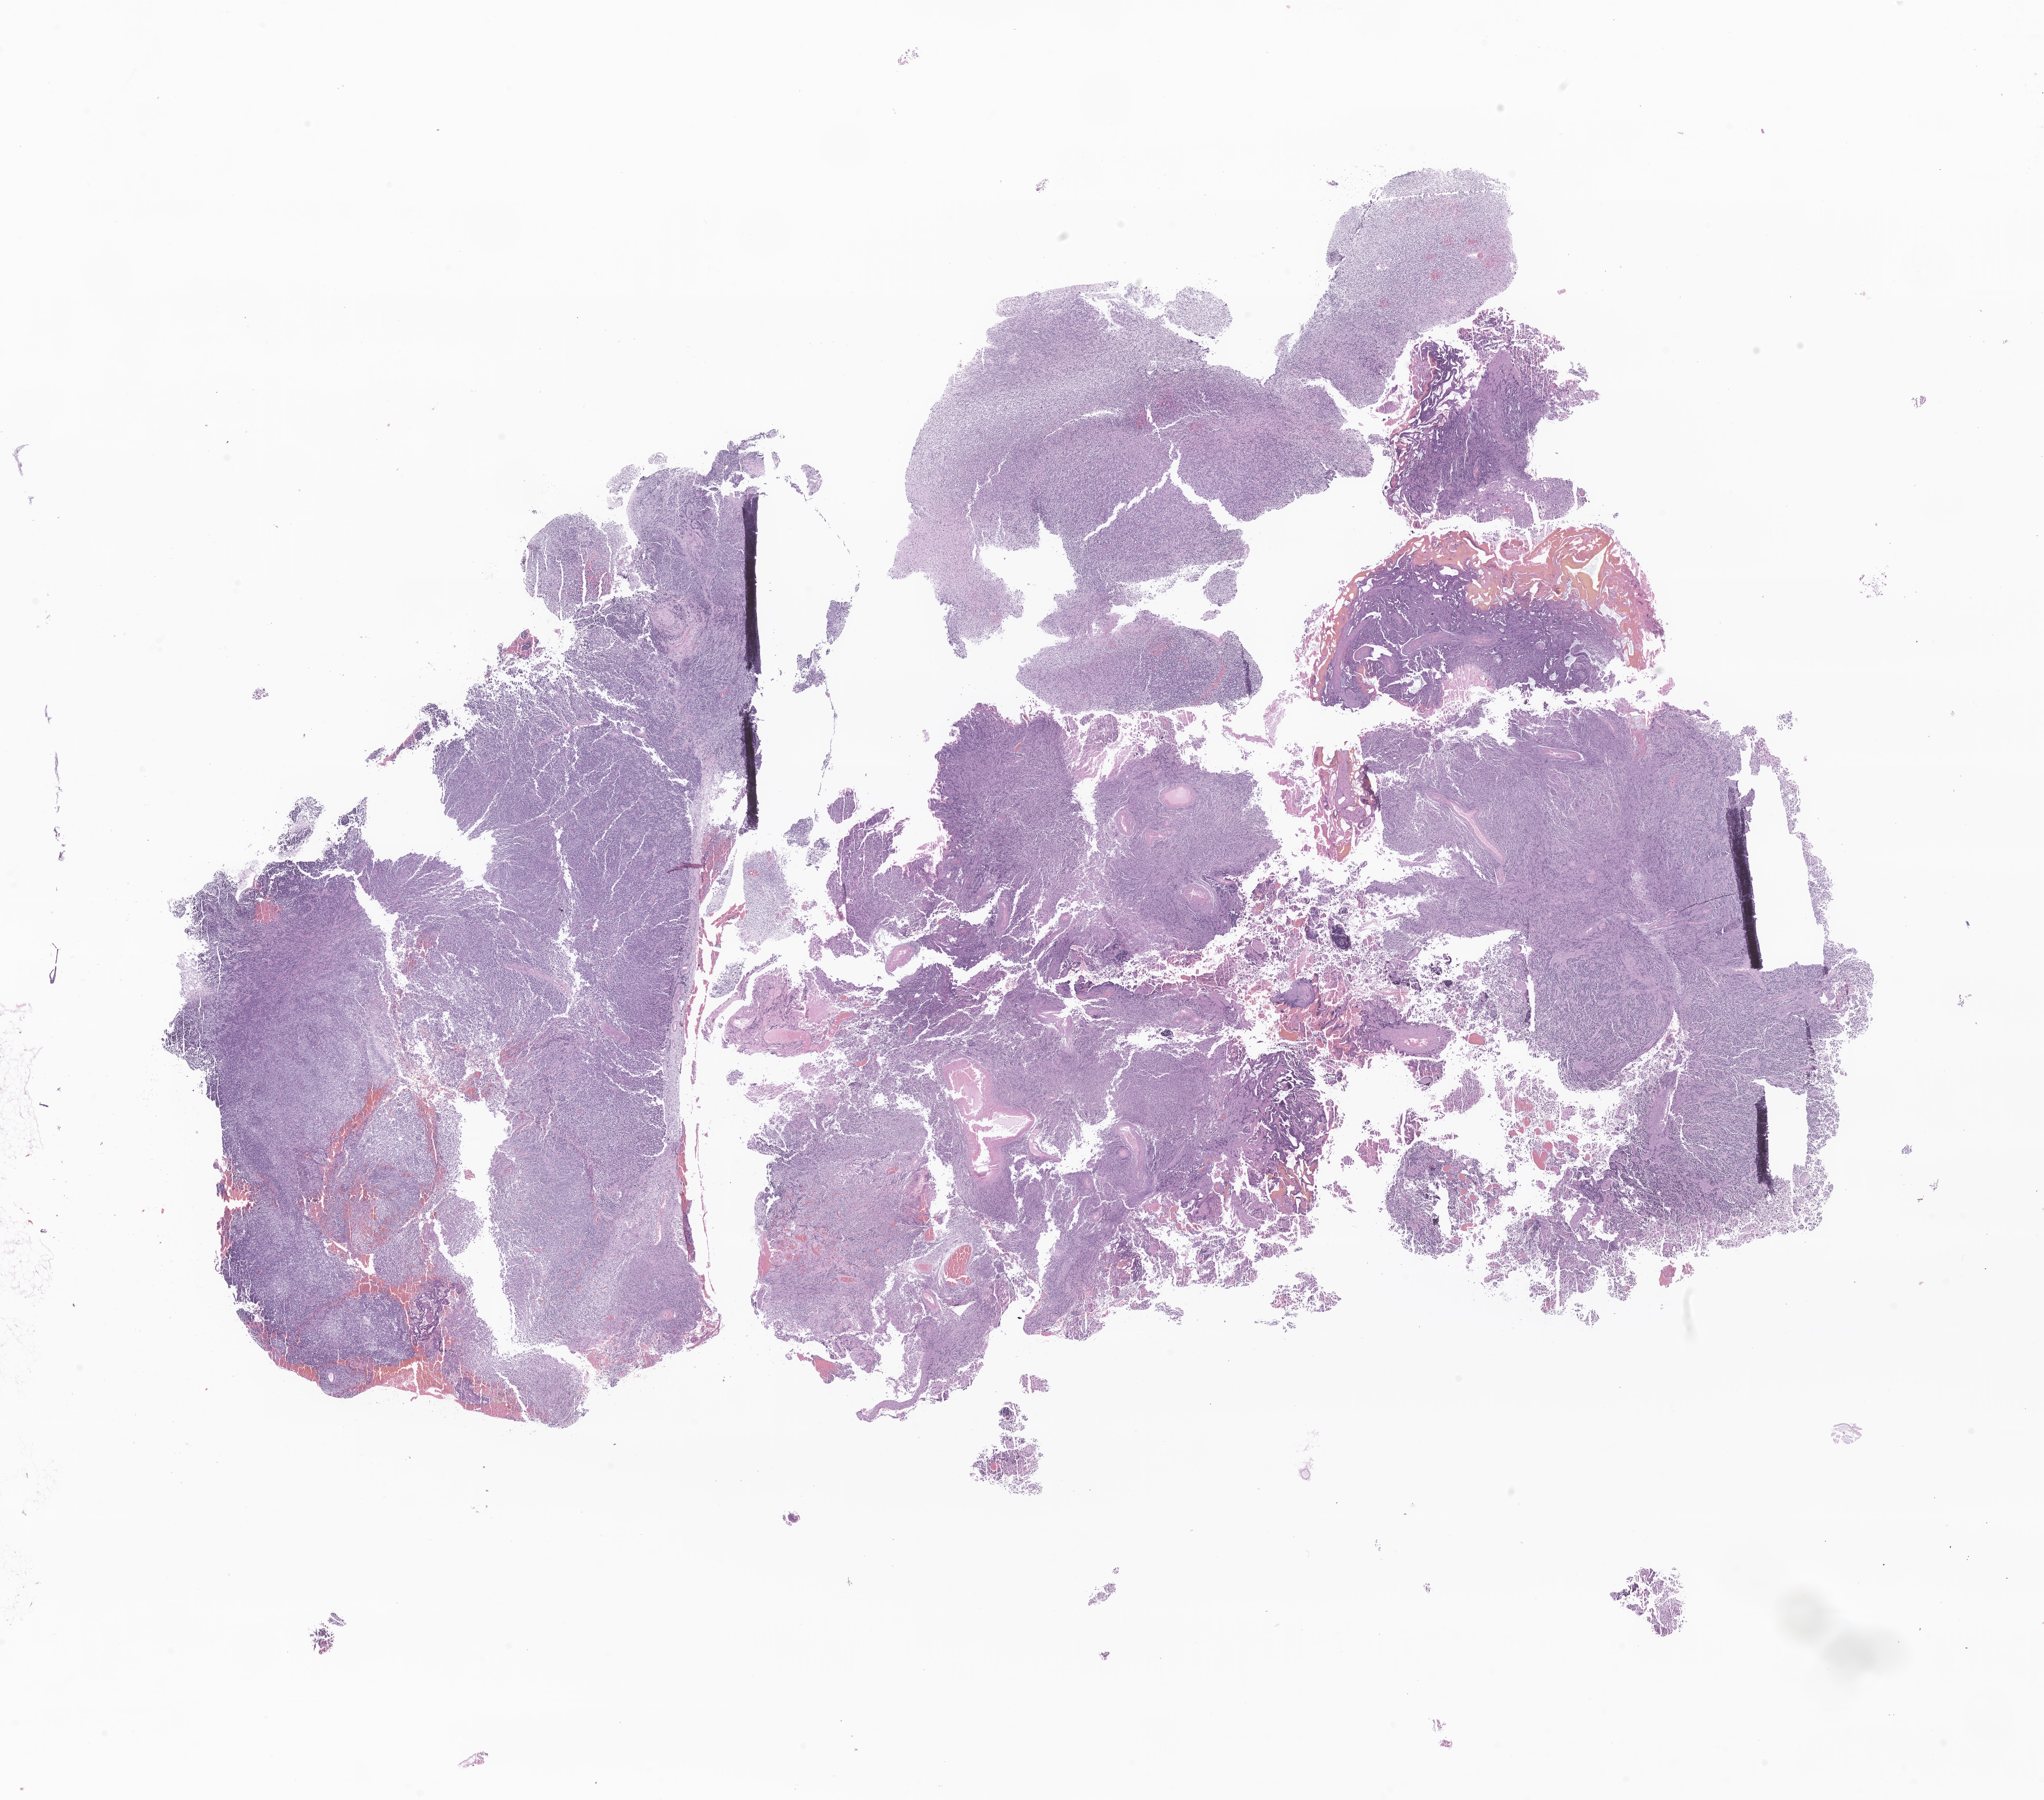
Digitized hematoxylin and eosin (H&E)-stained section of tumor tissue from the brain — low-resolution overview of the scanned area, about 23.2 x 20.4 mm; formalin-fixed, paraffin-embedded (FFPE) tissue. Patient: male, age 114 months (9 years 6 months).
* recorded diagnosis: Medulloblastoma, NOS